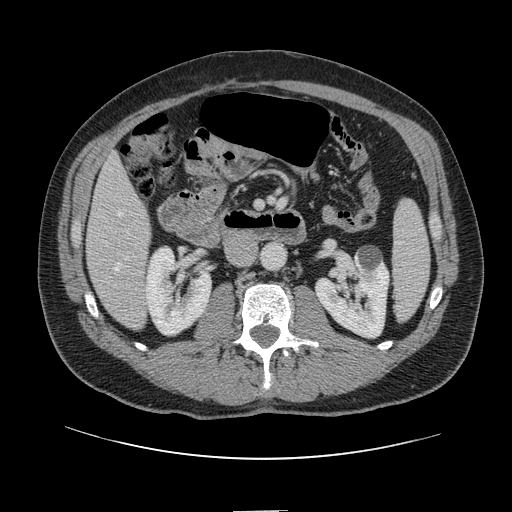
Contrast-enhanced abdominal CT, one axial slice. Slice 37 of 161 in the series (ordered by position). Intravenous contrast given. Soft-tissue window (W 400 / L 40 HU). 2.5 mm slice thickness. 512 × 512 image matrix. Male patient, age 66 years. From the clinical record (not read from this slice): diagnosis: colorectal cancer liver metastases, imaged before liver resection; multiple liver metastases: no; largest metastasis: 3.5 cm; disease in both lobes: no.
Structures marked on this image (manually delineated by an expert):
- hepatic veins: bounding box [x1, y1, x2, y2] px = [116, 212, 122, 272]
- liver: [87, 158, 151, 328]
- planned liver remnant (the part of the liver to remain after resection): [87, 158, 148, 266]